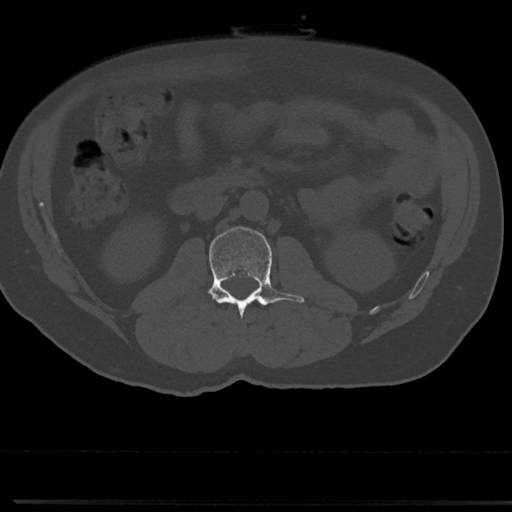
CT including the spine, one axial slice; position 14 of 817 along the scan axis; bone window (W 1800 / L 400 HU); 512 × 512 image matrix. Patient: male, 61 years. From the clinical record (not read from this slice): primary cancer: prostate.
Structures marked on this image (semi-automatically segmented with operator editing):
- L2 vertebra: bounding box (x1, y1, x2, y2) in pixels: (208, 227, 304, 322)